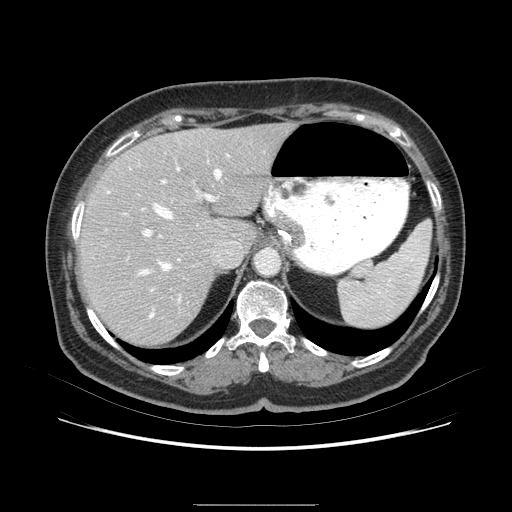
Contrast-enhanced abdominal CT (liver protocol), one axial slice; position 55 of 79 along the scan axis; 120 kVp; soft-tissue window (W 400 / L 40 HU); 512 × 512 image matrix. Case-level facts recorded for this patient, not image findings: diagnosis: hepatocellular carcinoma (patient treated with transarterial chemoembolisation; whether this scan precedes or follows treatment is not stated here); TNM stage (as recorded): Stage-I; Child-Pugh class: A; tumour nodularity: uninodular.
Outlined on this slice (semi-automatically segmented with operator editing):
- abdominal aorta: bounding box [x1, y1, x2, y2] px = [257, 250, 282, 277]
- liver parenchyma outside the tumour (the mass and vessels are separate outlines, so this box may not span the whole liver): [78, 128, 300, 336]
- liver vessels: [81, 159, 242, 285]